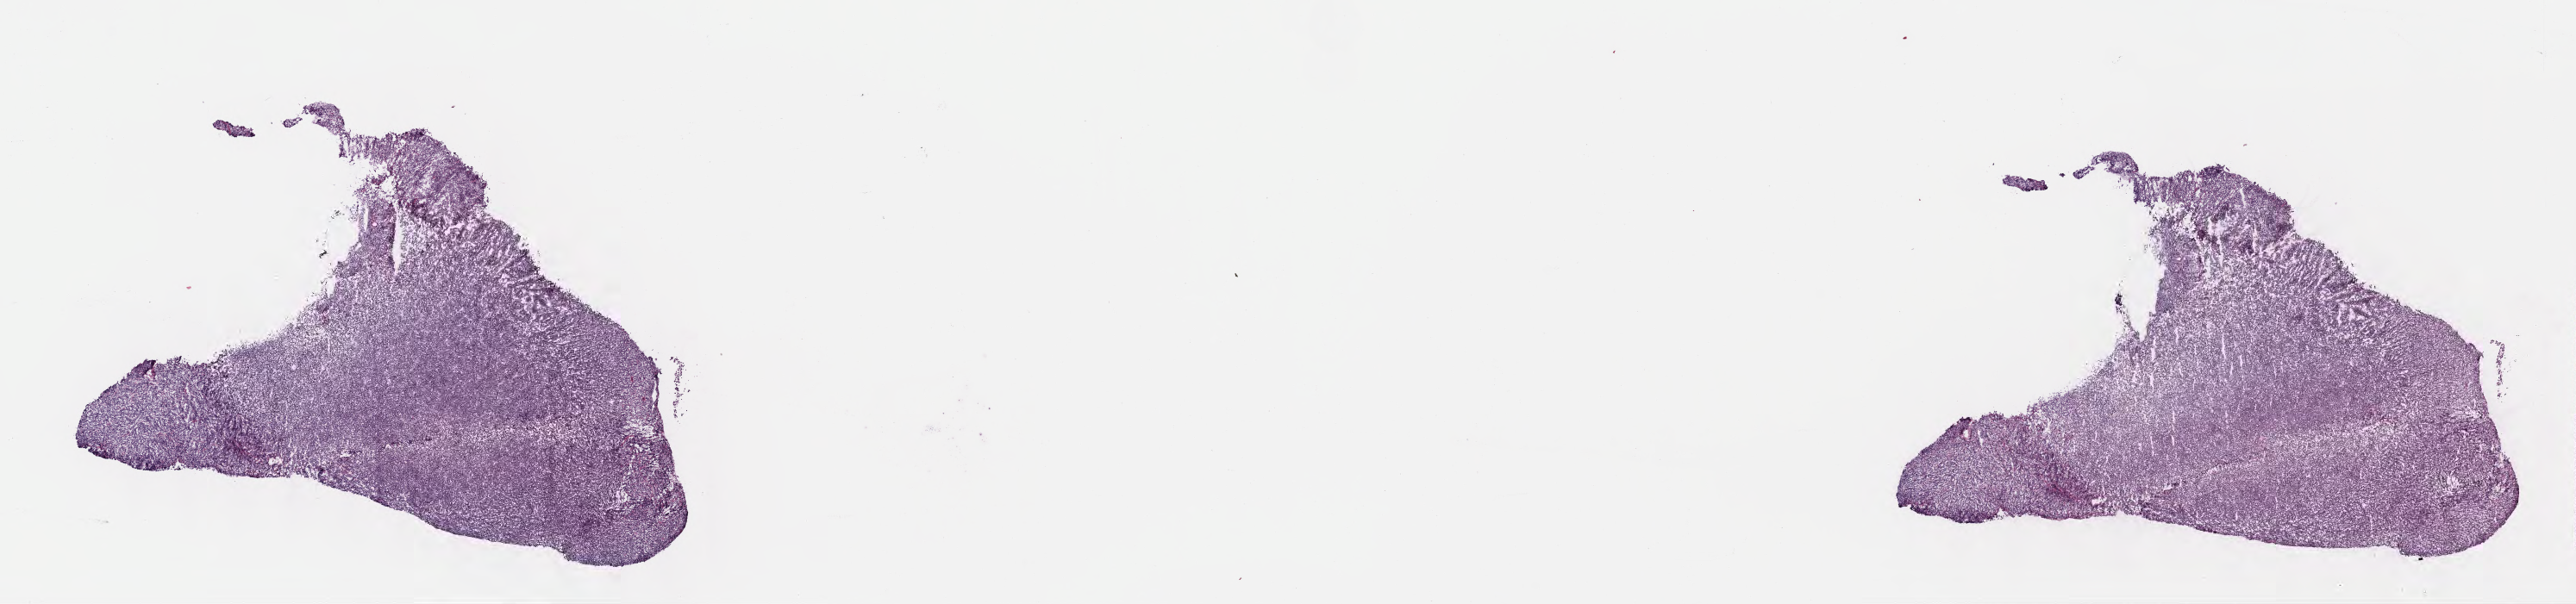
Whole-slide image, hematoxylin and eosin (H&E) stain, a low-resolution overview of the entire scanned area, about 24.1 x 5.7 mm. Frozen section. Specimen: primary tumor. Anatomic site: buccal mucosa. Female, age 7 years at initial diagnosis. Composition of this section per pathologist review: tumor cells 90%, tumor nuclei 90%, stromal cells 5%, necrosis 5%, normal cells 0%. Inflammatory infiltration, as recorded: lymphocyte infiltration 80%, monocyte infiltration 10%, neutrophil infiltration 0%.
- Ann Arbor stage (patient): Stage III
- histologic diagnosis: Burkitt lymphoma, NOS
- section: top of the tissue portion